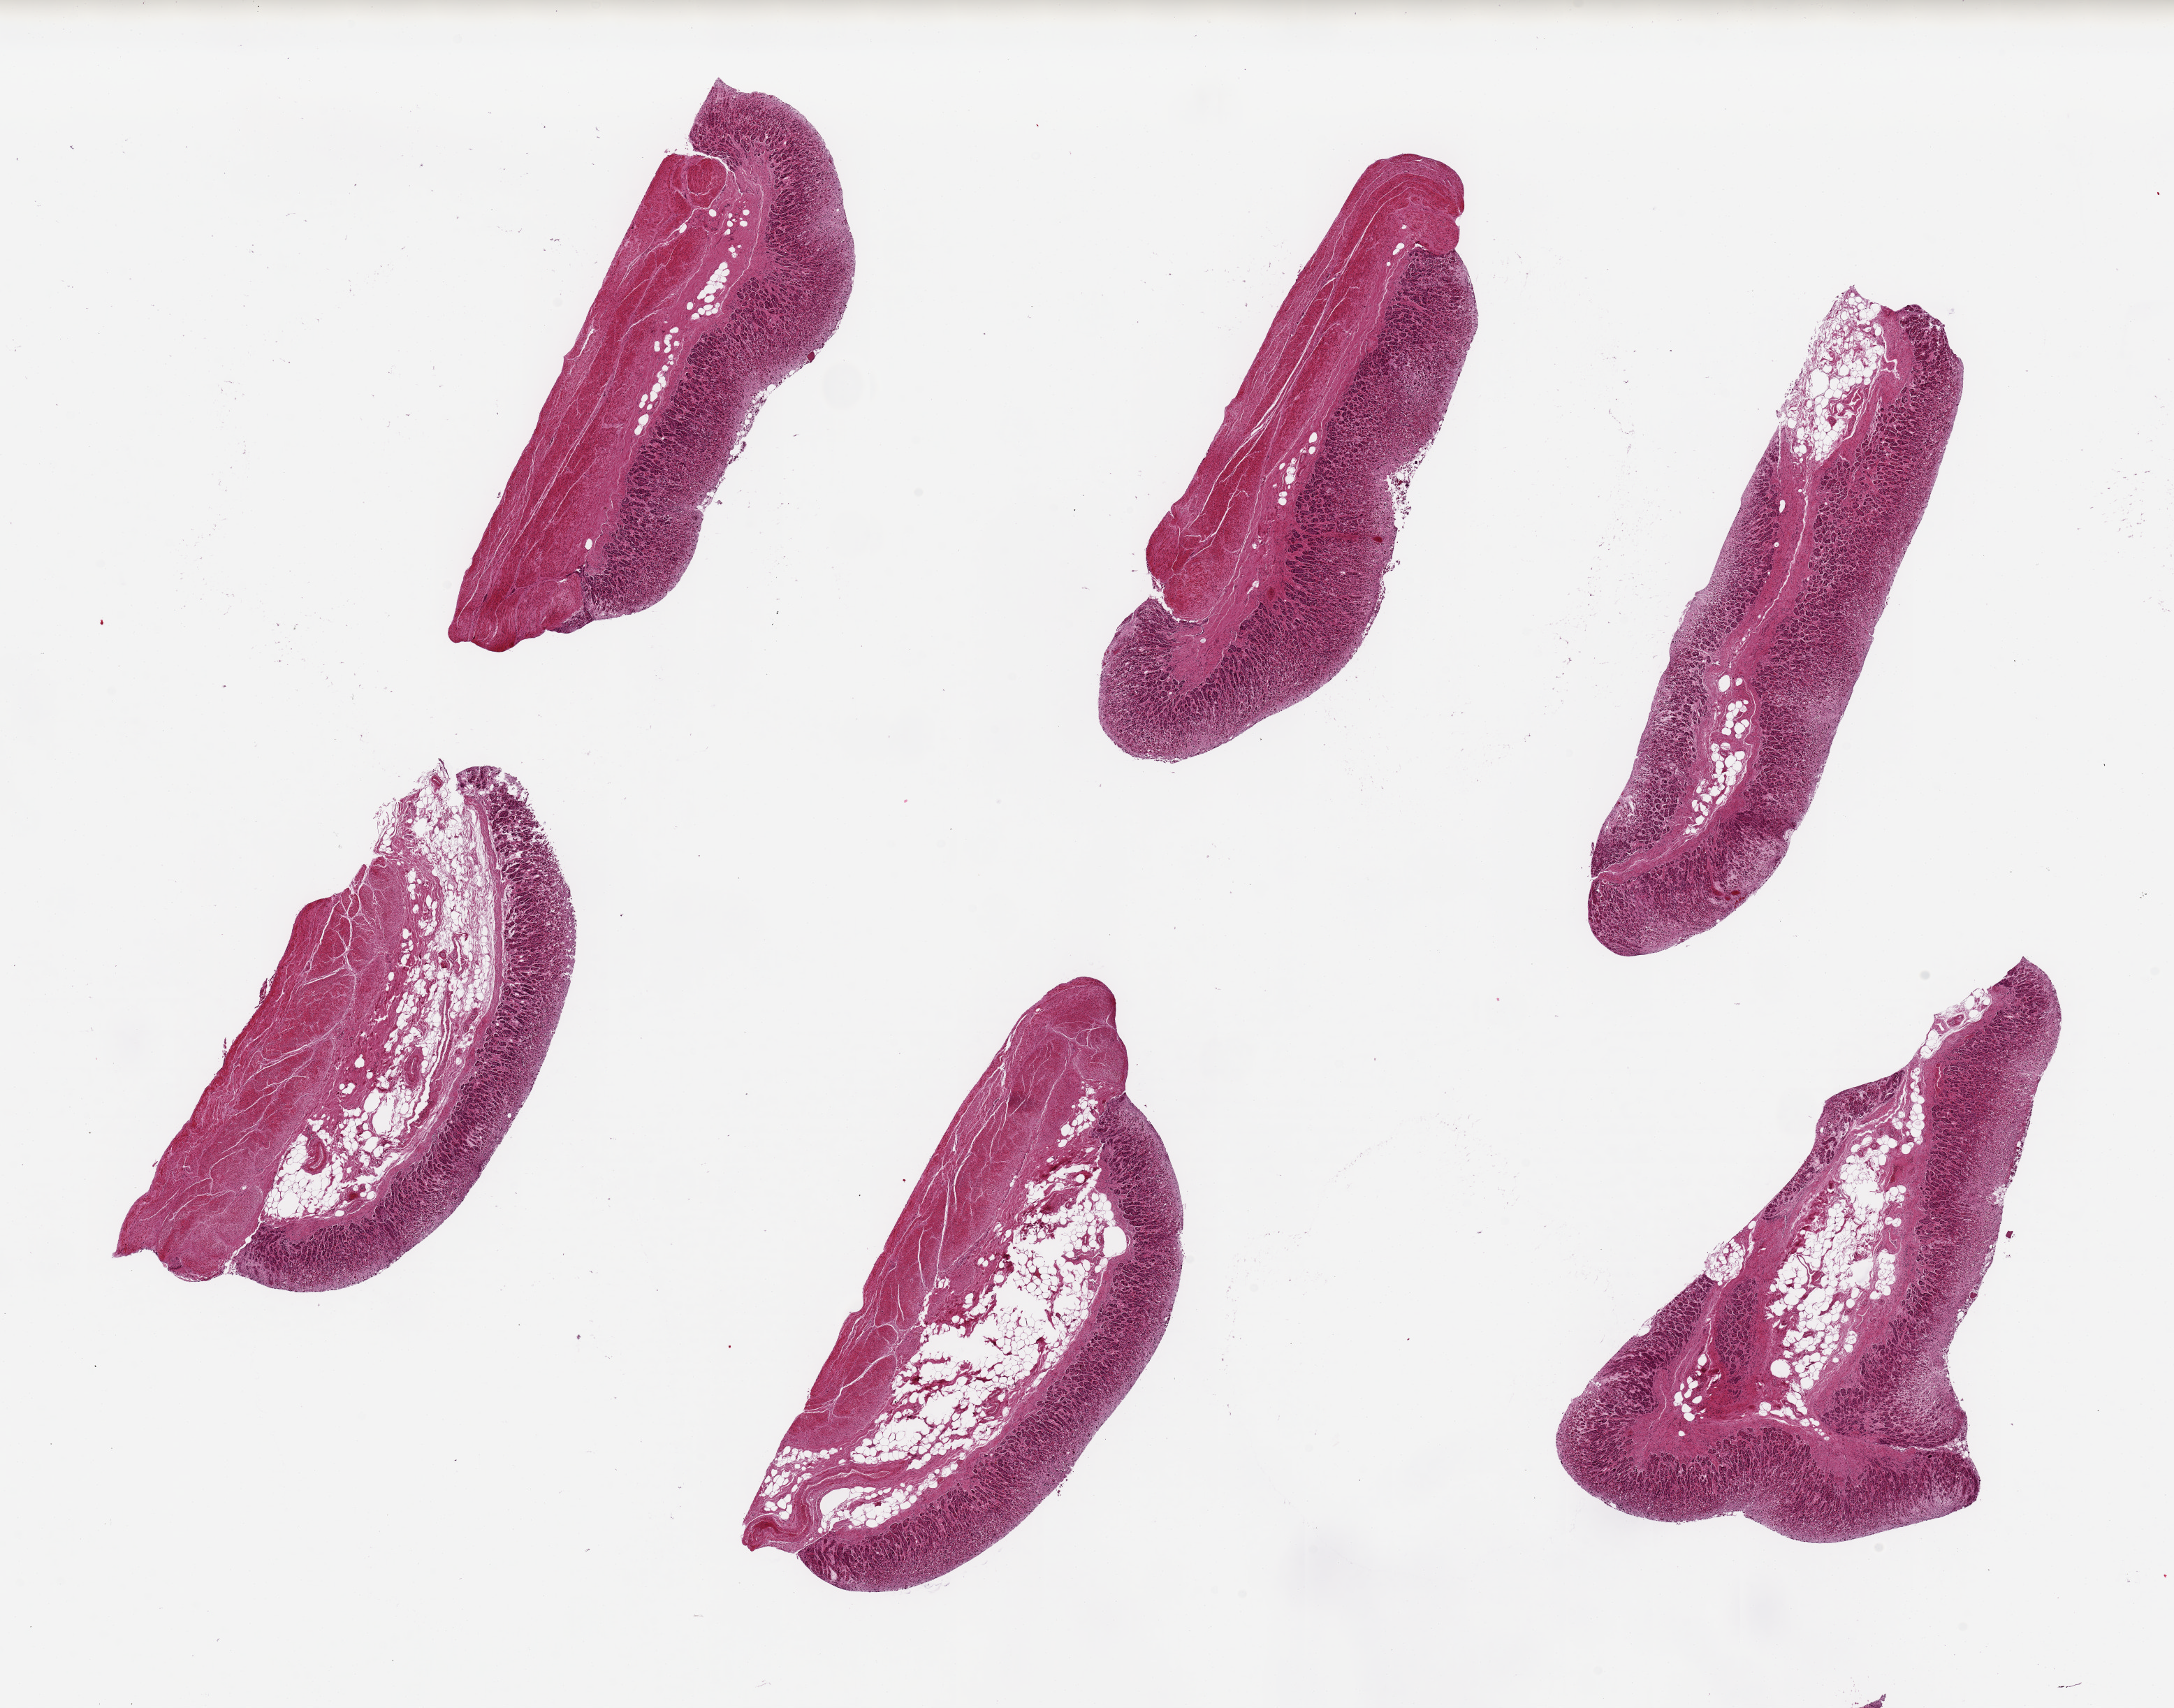
Hematoxylin and eosin (H&E) whole-slide image — shown as a low-resolution overview of the whole scanned area (about 24.6 x 19.3 mm), PAXgene-fixed, paraffin-embedded tissue, sampled site (target tissue): stomach, donor tissue sample. Donor sex: male.
* pathologist's review note for this sample: 6 pieces, 7x2.5mm. Mucosa is ~30-50% of thickness, poorly preserved